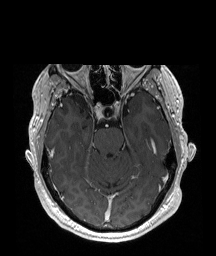
Brain MRI from a brain-tumour surgery series, one axial slice; position 127 of 192 along the scan axis; T1-weighted post-contrast; 216 × 256 image matrix, field of view 219 × 260 mm. Case-level facts recorded for this patient, not image findings: histopathology: Astrocytoma; WHO grade: 2; IDH mutation: yes.
Annotated regions visible in this slice (manually delineated by an expert):
- tumour: bounding box <68,94,90,113> (left, top, right, bottom; pixels)